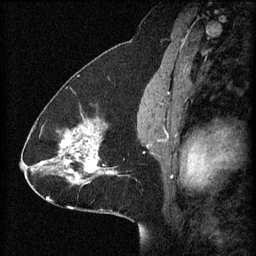
Breast MRI (dynamic contrast-enhanced), one sagittal slice; position 35 of 60 along the scan axis; 3 images stored at this slice position (order not interpretable as contrast timing); 1.5 T; TE 4.2 ms, TR 8.2 ms; 256 × 256 image matrix. Patient: female, 41 years.
Annotated regions visible in this slice (semi-automatic segmentation, software-assisted and operator-edited):
- analysis volume of interest (the breast-tissue region the enhancement analysis was run in; not a lesion): box from (x=58, y=110) to (x=128, y=181) px
- tumour enhancement mask (voxels above the 70 % enhancement threshold inside the analysis volume of interest): (x=59, y=120)–(x=116, y=181)